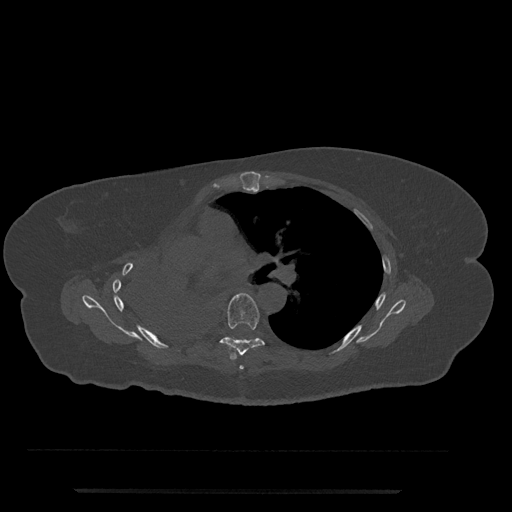
CT including the spine, one axial slice. Slice 494 of 797 in the series (ordered by position). Reconstruction kernel Br40s/3. Bone window (W 1800 / L 400 HU). 512 × 512 image matrix, field of view 440 × 440 mm. Patient: female, 51 years. From the clinical record (not read from this slice): primary cancer: neuro.
Outlined on this slice (semi-automatically segmented with operator editing):
- T5 vertebra: bounding box (x1, y1, x2, y2) in pixels: (239, 365, 244, 370)
- T6 vertebra: (220, 293, 265, 360)